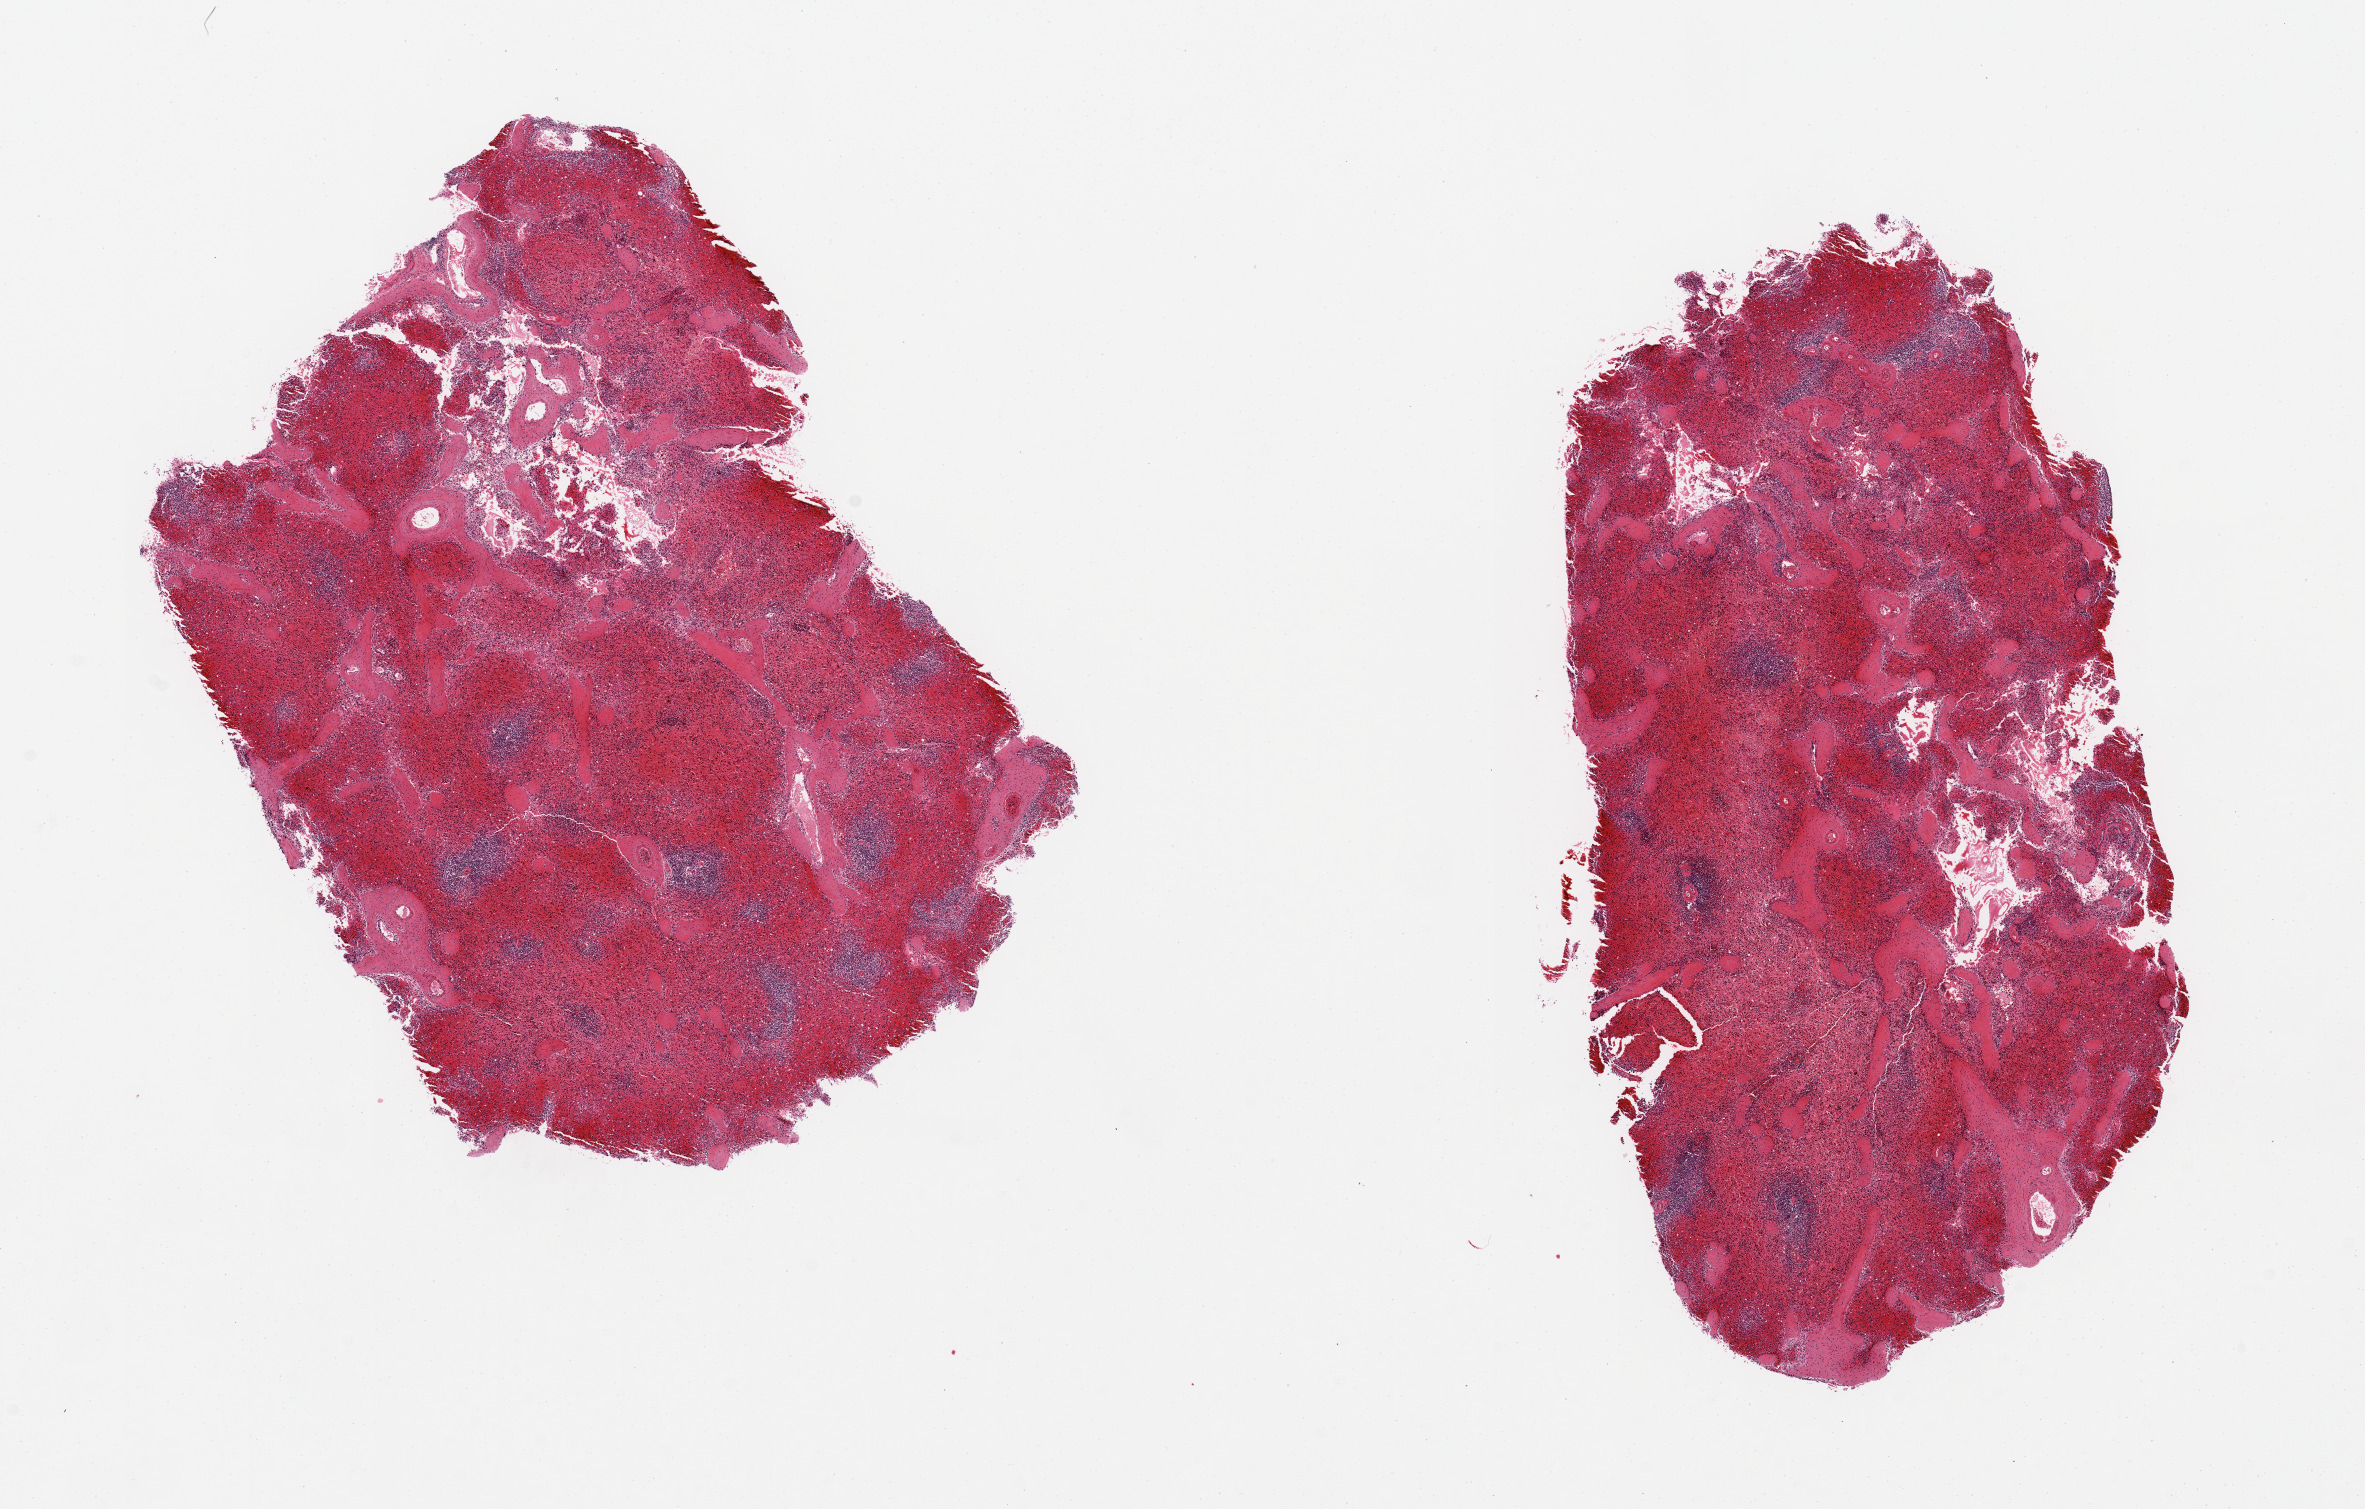
H&E whole-slide image — low-resolution overview of the scanned area, about 18.7 x 11.9 mm (from a 20x scan); PAXgene-fixed, paraffin-embedded tissue; section of spleen (target tissue); donor tissue sample. Donor: female.
Pathologist's review note for this sample: 2 pieces, marked congestion/autolyzed.